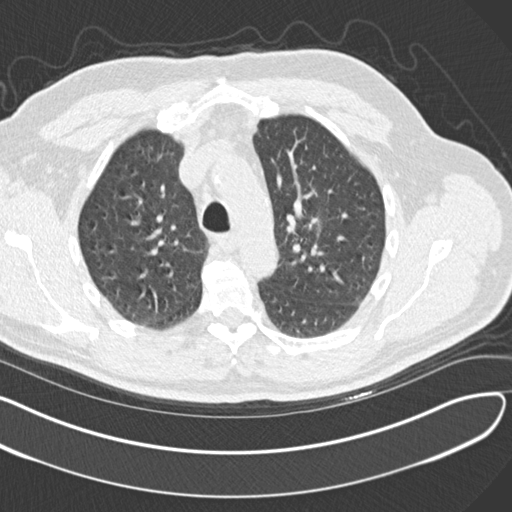
Chest CT (low-dose screening protocol), one axial image; second annual screen; lung window (W 1500 / L -600 HU); standard (soft-tissue) reconstruction kernel (B30f); 120 kVp; 512 × 512 image matrix, field of view 372 × 372 mm. Male participant, aged 65 years at enrolment. Former smoker at enrolment.
Expert-annotated lung lesion, bounding box (x1, y1, x2, y2) in pixels: (283, 197, 337, 258). The screening reader recorded 4 non-calcified nodules or masses ≥4 mm on this exam (left upper lobe, left upper lobe, left lower lobe, right middle lobe); which of them this box marks is not recorded. Later outcome: lung cancer diagnosed 577 days after this screen (after the third annual screen) — acinar cell carcinoma, left upper lobe, stage IA (AJCC 6th edition), 25 mm at pathology.